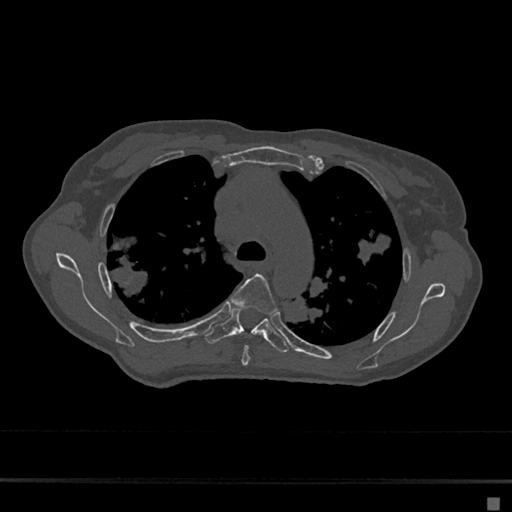
CT including the spine, one axial slice. Slice 481 of 797 in the series (ordered by position). Reconstruction kernel Br40s/3. Bone window (W 1800 / L 400 HU). 0.5 mm slice thickness. 512 × 512 image matrix. Female patient, age 68 years. From the clinical record (not read from this slice): primary cancer: renal.
Outlined on this slice (semi-automatically segmented with operator editing):
- T4 vertebra: bounding box [x1, y1, x2, y2] px = [231, 273, 278, 366]
- T5 vertebra: [205, 308, 289, 353]